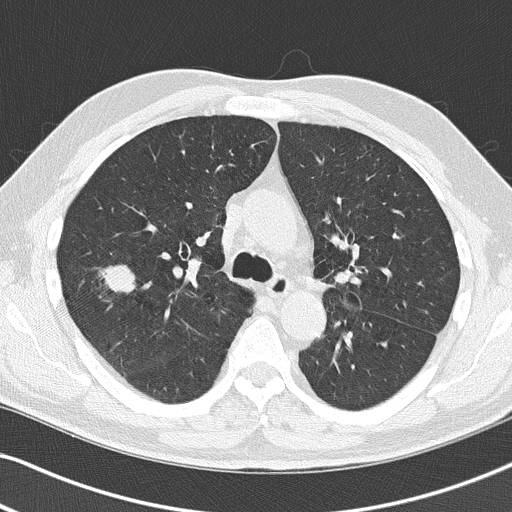
Low-dose screening chest CT, one axial slice; slice 87 of 140 in the series (ordered by position); 120 kVp; lung window (W 1500 / L -600 HU); 2 mm slice thickness; 512 × 512 image matrix, field of view 330 × 330 mm.
Outlined on this slice (manually delineated by an expert):
- lesion 1 (tumor, upper lobe of right lung): bounding box [x1, y1, x2, y2] px = [102, 265, 135, 292]